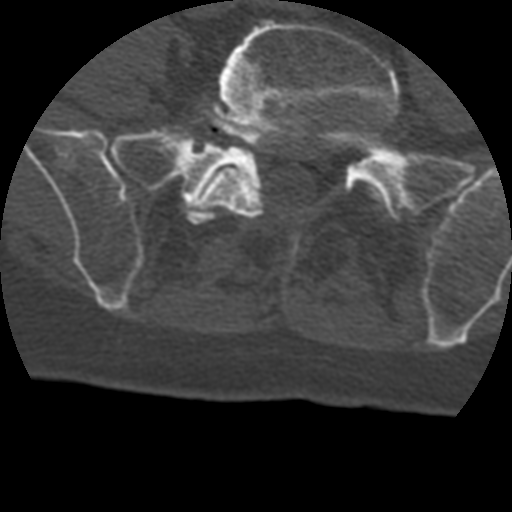
CT including the spine, one axial slice. Reconstruction kernel STANDARD. Bone window (W 1800 / L 400 HU). 1.25 mm slice thickness. 512 × 512 image matrix. Patient age 69 years. Case-level facts recorded for this patient, not image findings: primary cancer: prostate.
Outlined on this slice (semi-automatically segmented with operator editing):
- L5 vertebra: bounding box <184,19,400,217> (left, top, right, bottom; pixels)